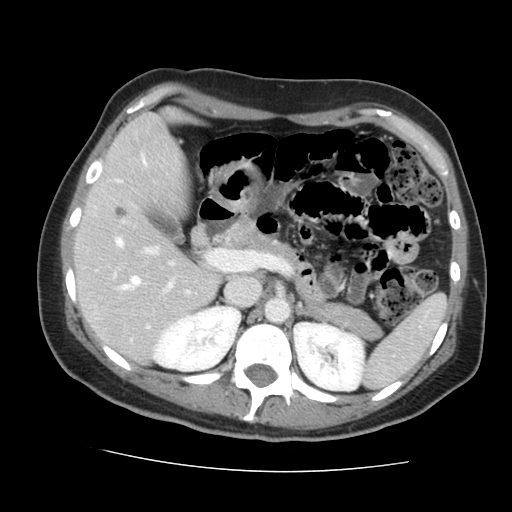
Contrast-enhanced abdominal CT, one axial slice. 120 kVp. Intravenous contrast given. Soft-tissue window (W 400 / L 40 HU). 2.5 mm slice thickness. 512 × 512 image matrix, field of view 333 × 333 mm. Female patient, age 46 years. Case-level facts recorded for this patient, not image findings: diagnosis: colorectal cancer liver metastases, imaged before liver resection; multiple liver metastases: no; largest metastasis: 2.8 cm; chemotherapy before resection: yes.
Annotated regions visible in this slice (expert manual segmentation):
- hepatic veins: bounding box <117,156,146,289> (left, top, right, bottom; pixels)
- liver: <77,116,218,359>
- planned liver remnant (the part of the liver to remain after resection): <77,116,218,359>
- portal vein (with intrahepatic branches): <114,239,226,293>
- liver metastasis: <114,206,127,222>